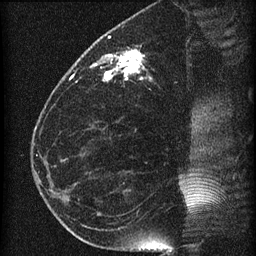
Breast MRI (dynamic contrast-enhanced), one sagittal slice; position 25 of 60 along the scan axis; dynamic contrast-enhanced series, image 2 of 4 at this slice position (ordered by acquisition); 1.5 T; TE 4.2 ms, TR 22.7 ms; 1.5 mm slice thickness; 256 × 256 image matrix, field of view 180 × 180 mm. Patient: female, 35 years. From the clinical record (not read from this slice): setting: breast cancer imaged before/during neoadjuvant chemotherapy; receptor status: HR-positive, HER2-negative.
Annotated regions visible in this slice (semi-automatic segmentation, software-assisted and operator-edited):
- analysis volume of interest (the breast-tissue region the enhancement analysis was run in; not a lesion): bounding box <69,27,199,112> (left, top, right, bottom; pixels)
- tumour enhancement mask (voxels above the 90 % enhancement threshold inside the analysis volume of interest): <69,49,142,81>